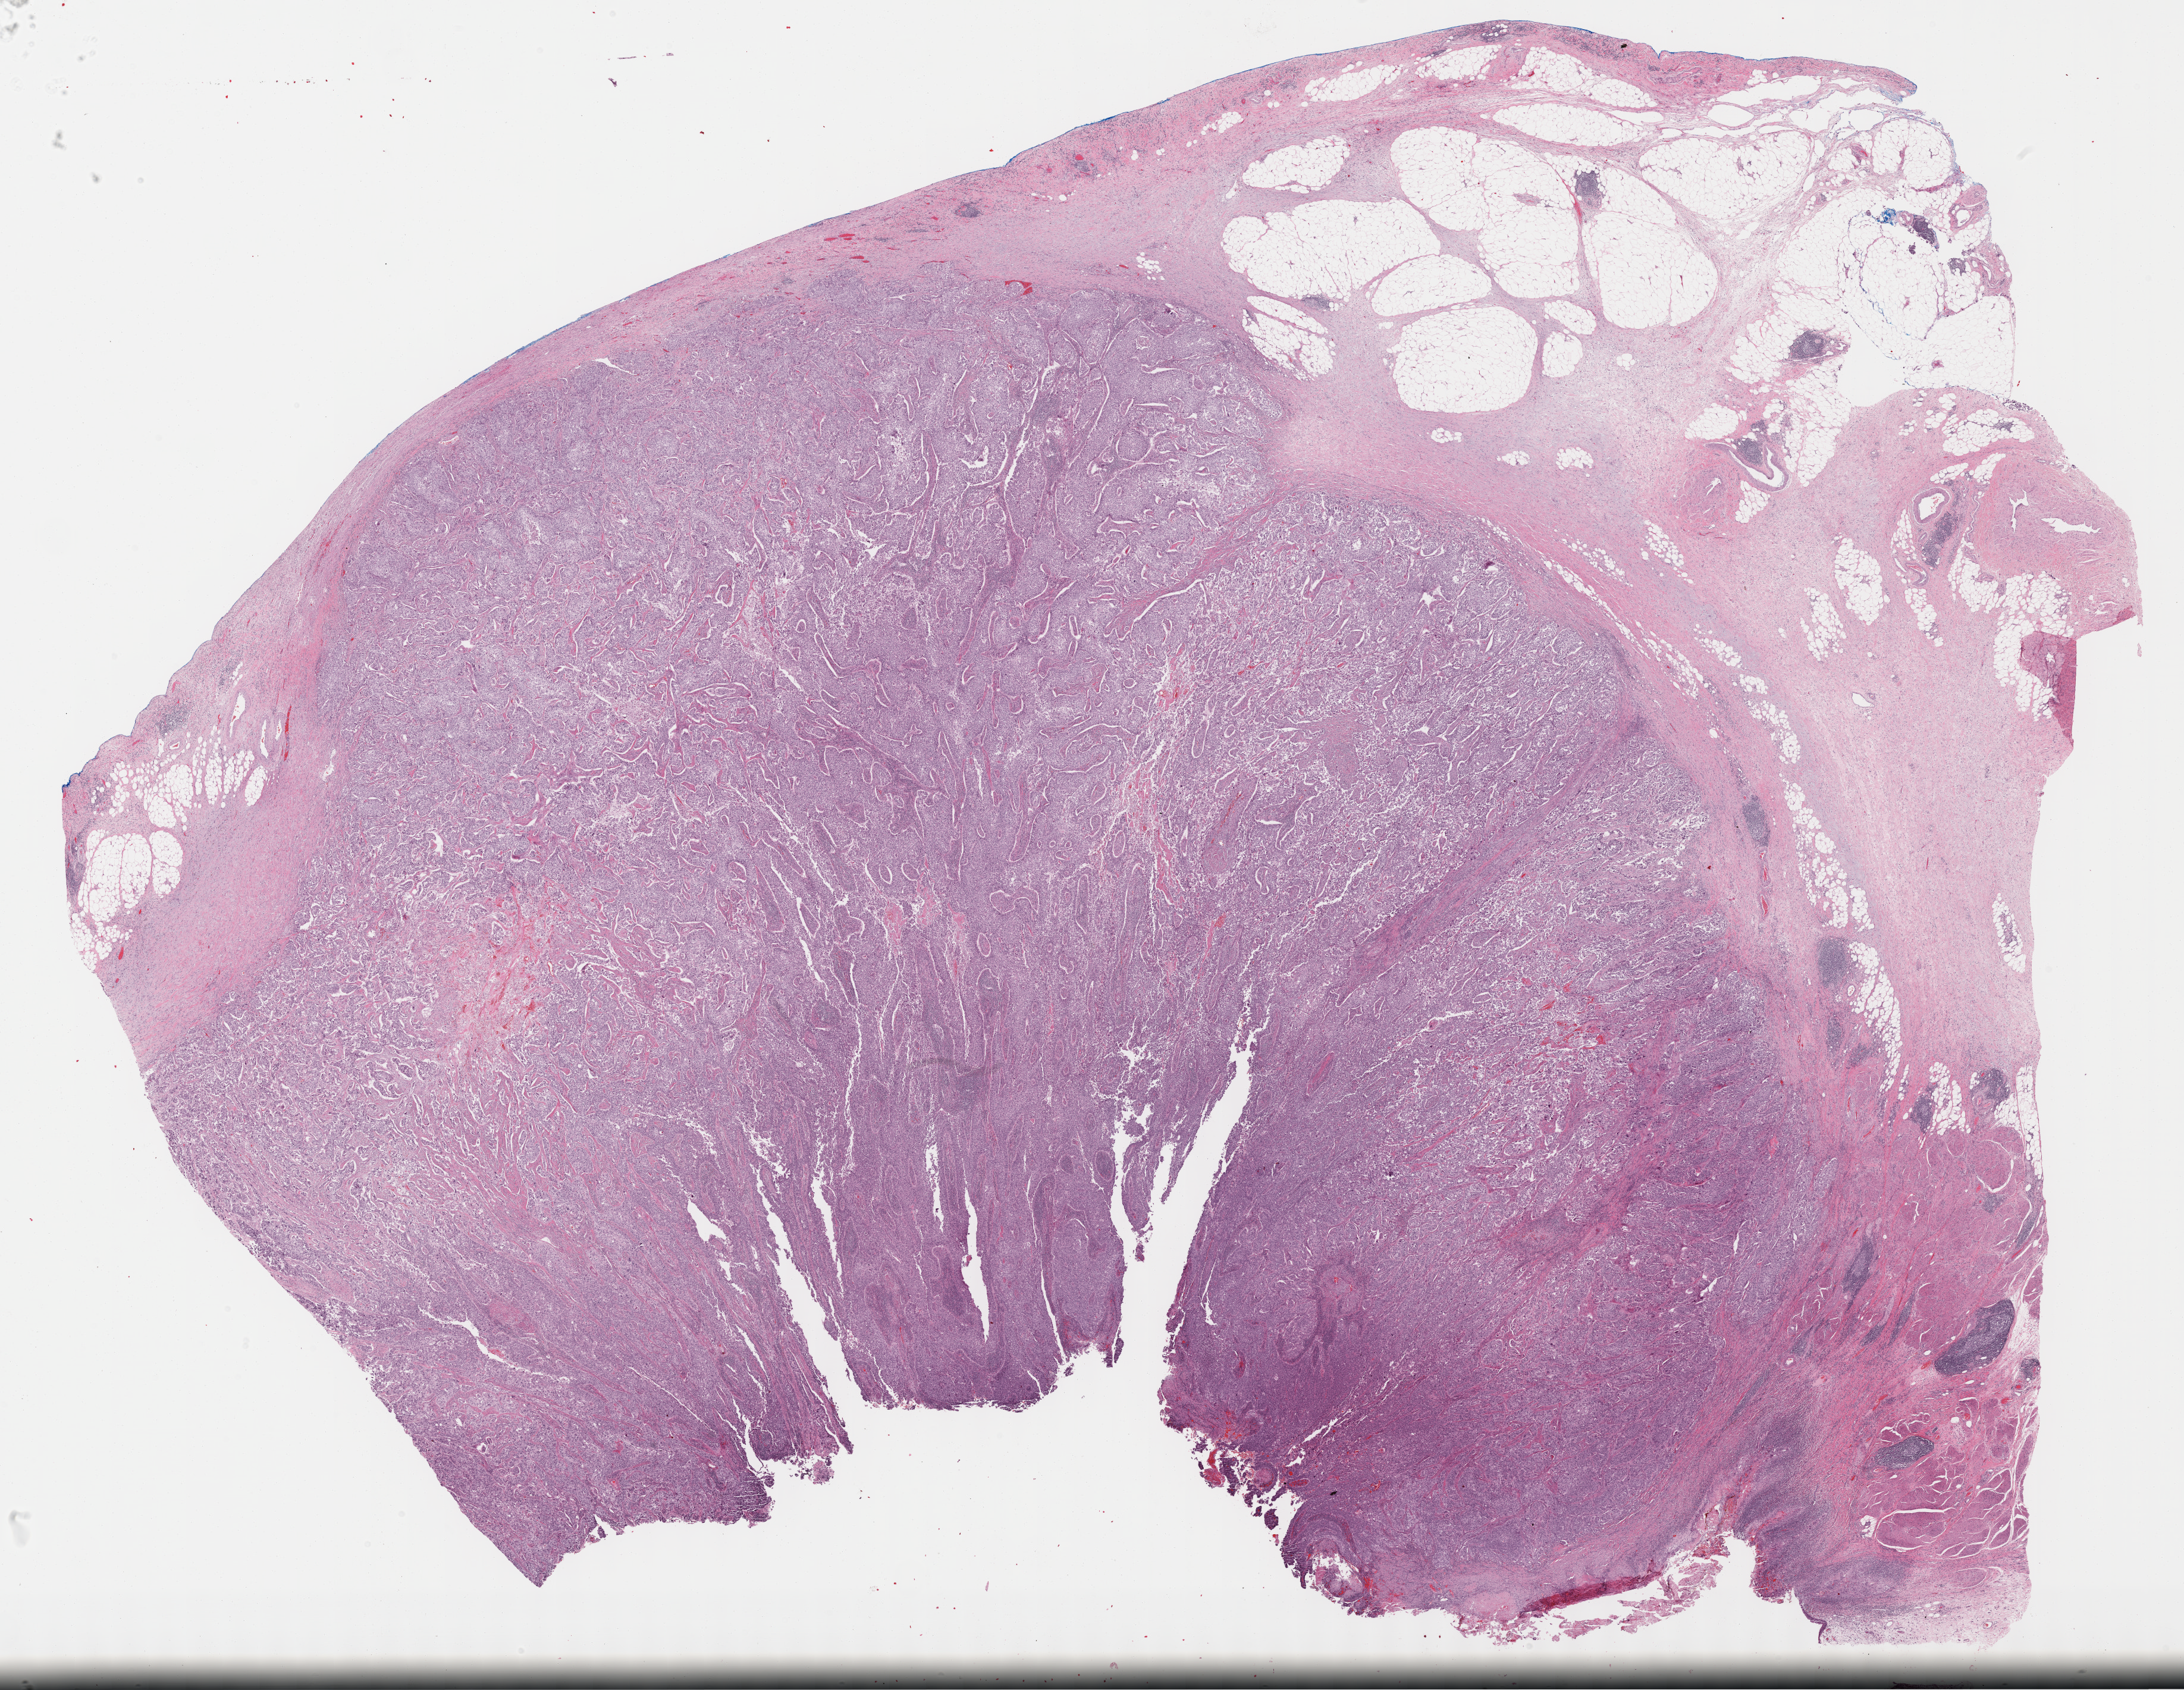
Digitized H&E tissue section (whole slide) — low-resolution overview of the scanned area, about 29.7 x 23.0 mm. Formalin-fixed paraffin-embedded (FFPE) diagnostic section. Sample: primary tumour, bladder. Female patient; age at initial diagnosis 78 years. Histologic grade: high grade.
Lymph nodes positive (case pathology): 0 of 19 examined. AJCC pathologic stage: III. Histologic diagnosis: Transitional cell carcinoma (dome of bladder).